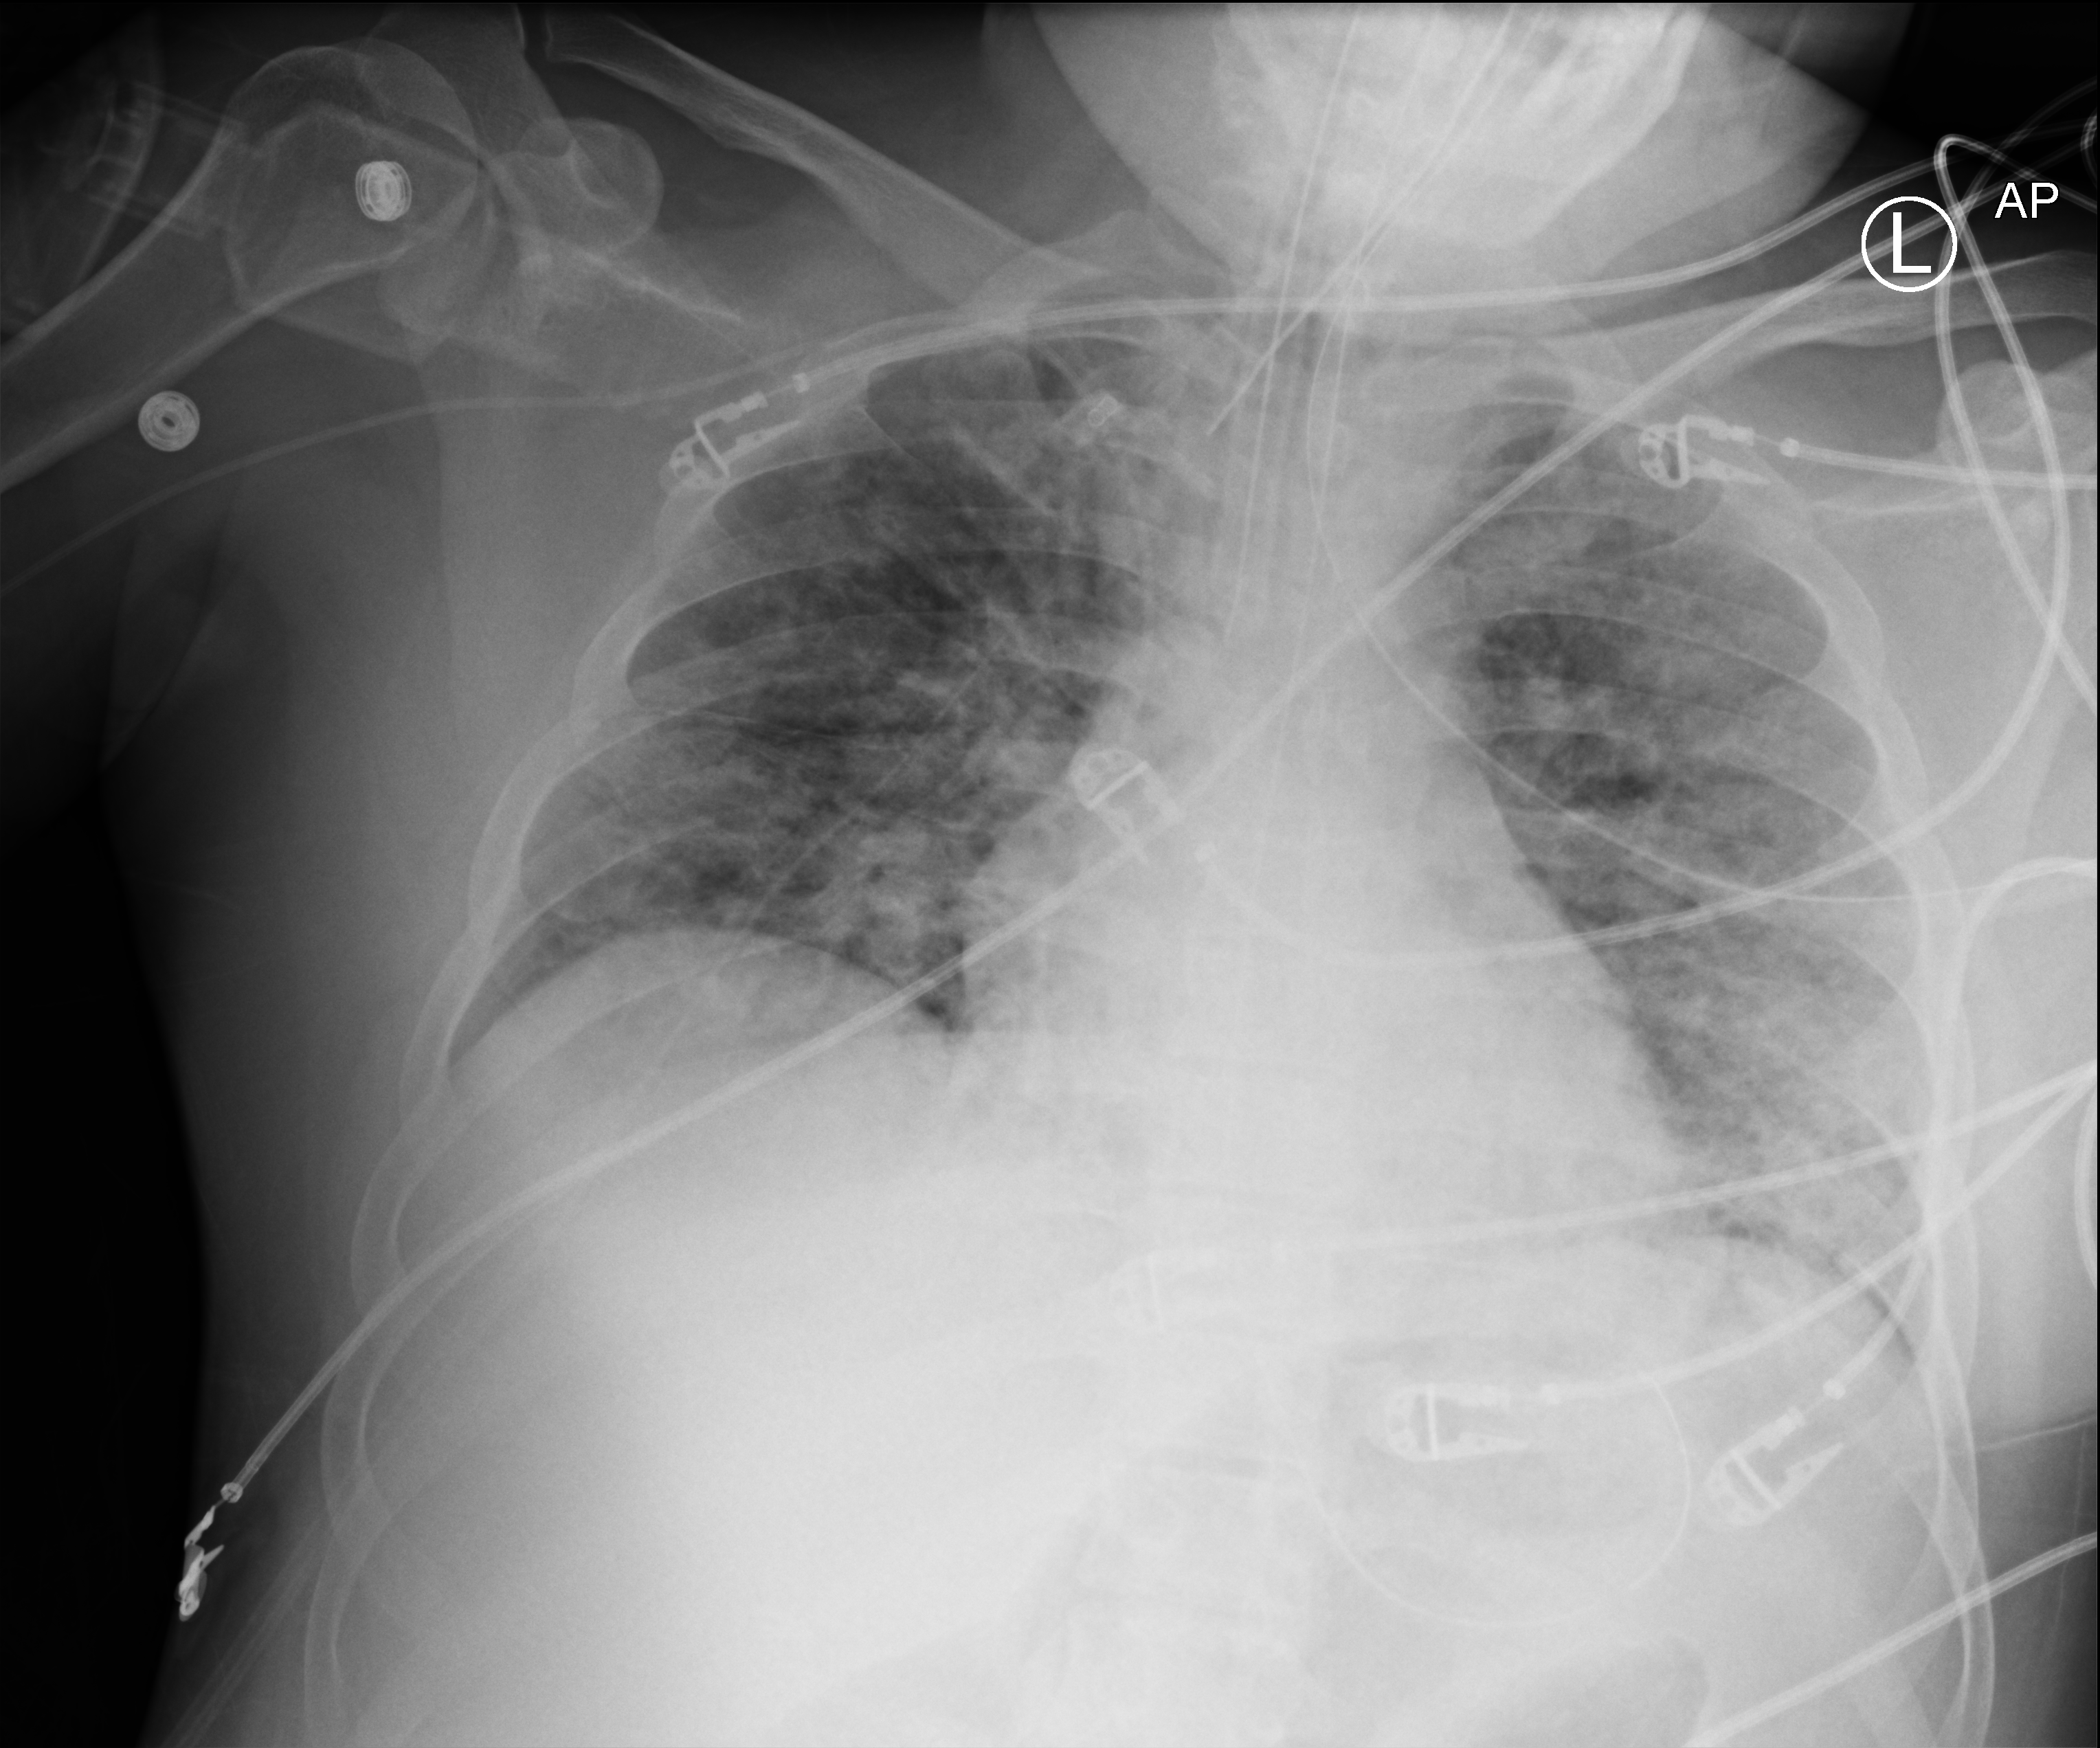
Chest X-ray (portable), anteroposterior (AP) projection. Male patient hospitalised with COVID-19, age 18–59 years.
Hospital-stay facts (about this admission, not read from this image; timing relative to this image not recorded):
- hypertension (admission record): no
- smoking status (admission record): former
- length of hospital stay: 44 days